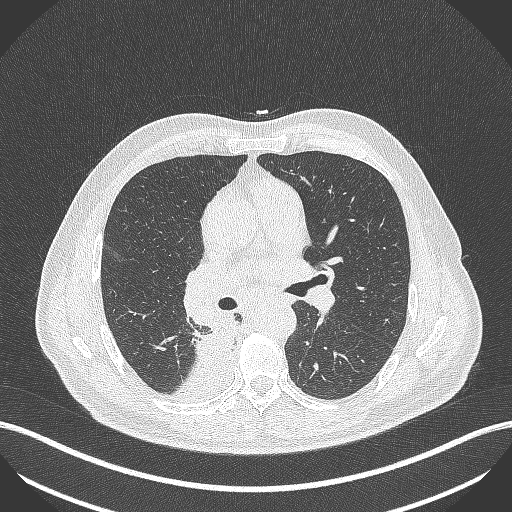
Chest CT, one axial slice; slice 266 of 451 in the series (ordered by position); 100 kVp; lung window (W 1500 / L -600 HU); 1 mm slice thickness; 512 × 512 image matrix. Male patient, age 61 years. Case-level facts recorded for this patient, not image findings: clinical TNM (as recorded): T1 N0 M0; histopathological grade: G3.
Structures marked on this image (bounding box drawn by a radiologist):
- lung tumour (recorded histology: small cell carcinoma): box from (x=192, y=308) to (x=245, y=373) px